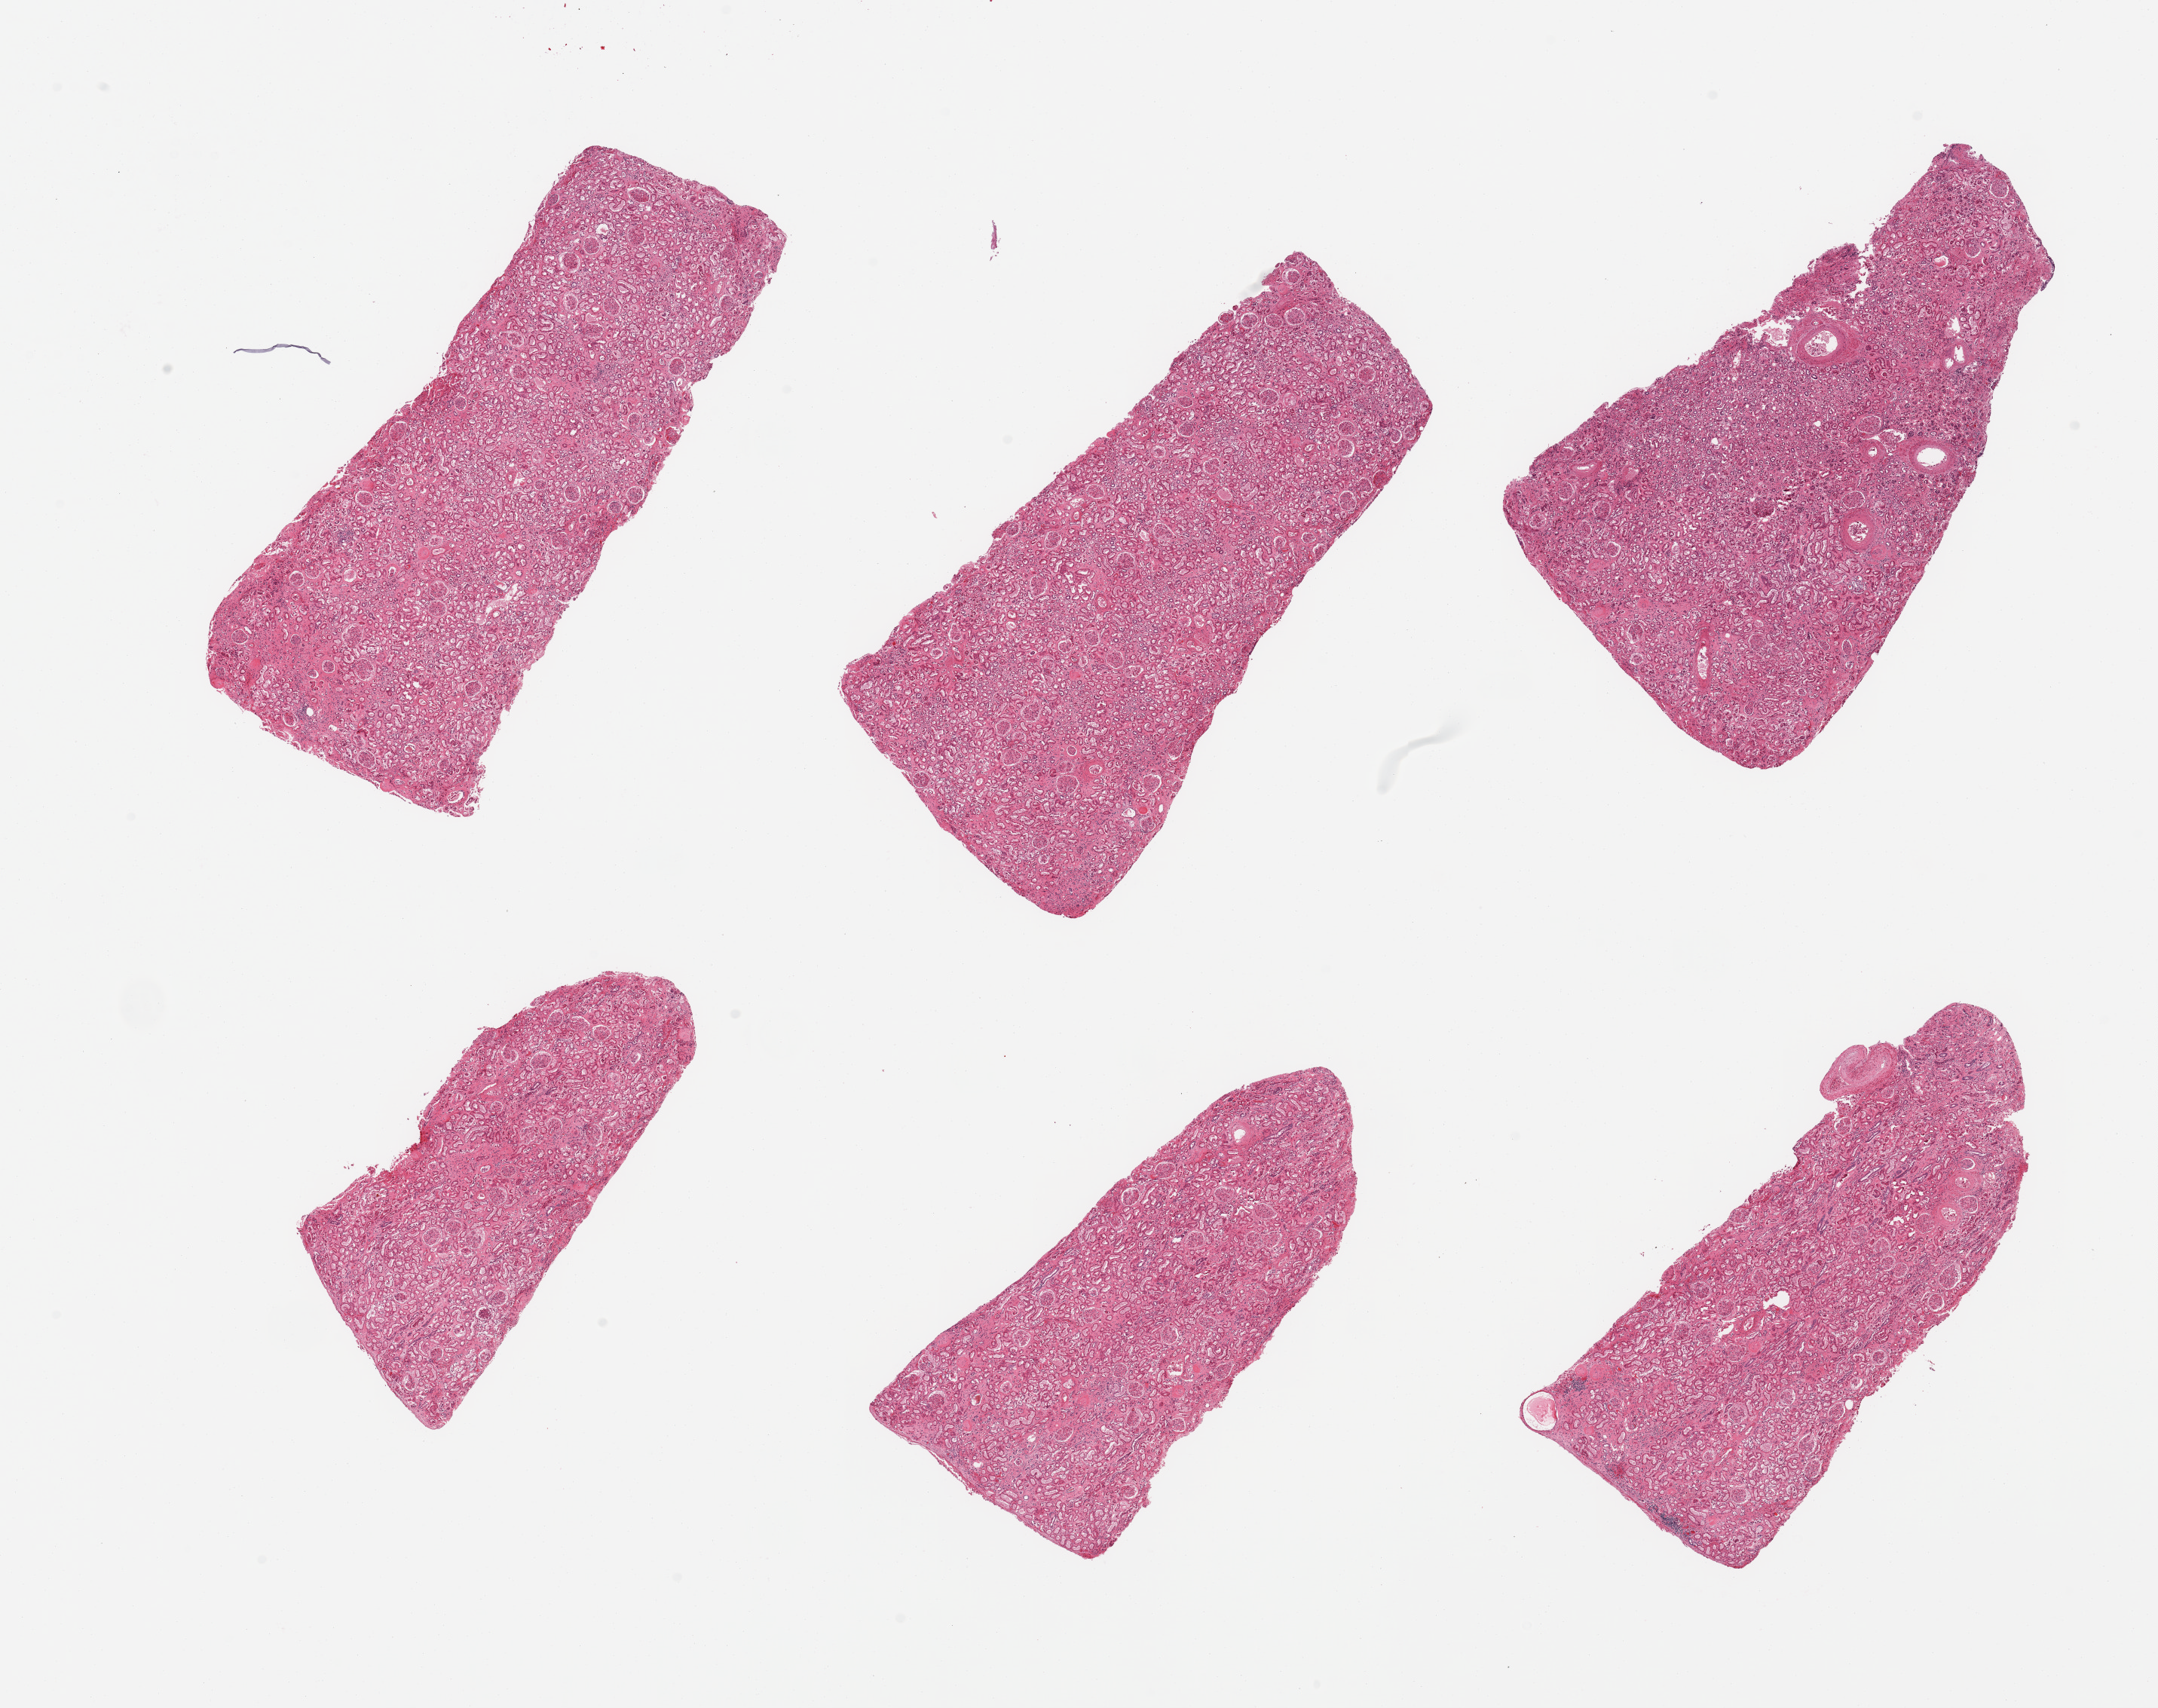
Digitized haematoxylin and eosin-stained section — whole scanned area (about 22.6 x 17.9 mm) shown as a low-resolution overview, PAXgene-fixed paraffin-embedded (PFPE) section, sampled site (target tissue): renal cortex, tissue donor sample. Male donor.
Reviewer comment on this tissue sample: 6 pieces, glomeruli present, tubules with mild-moderate autolysis.